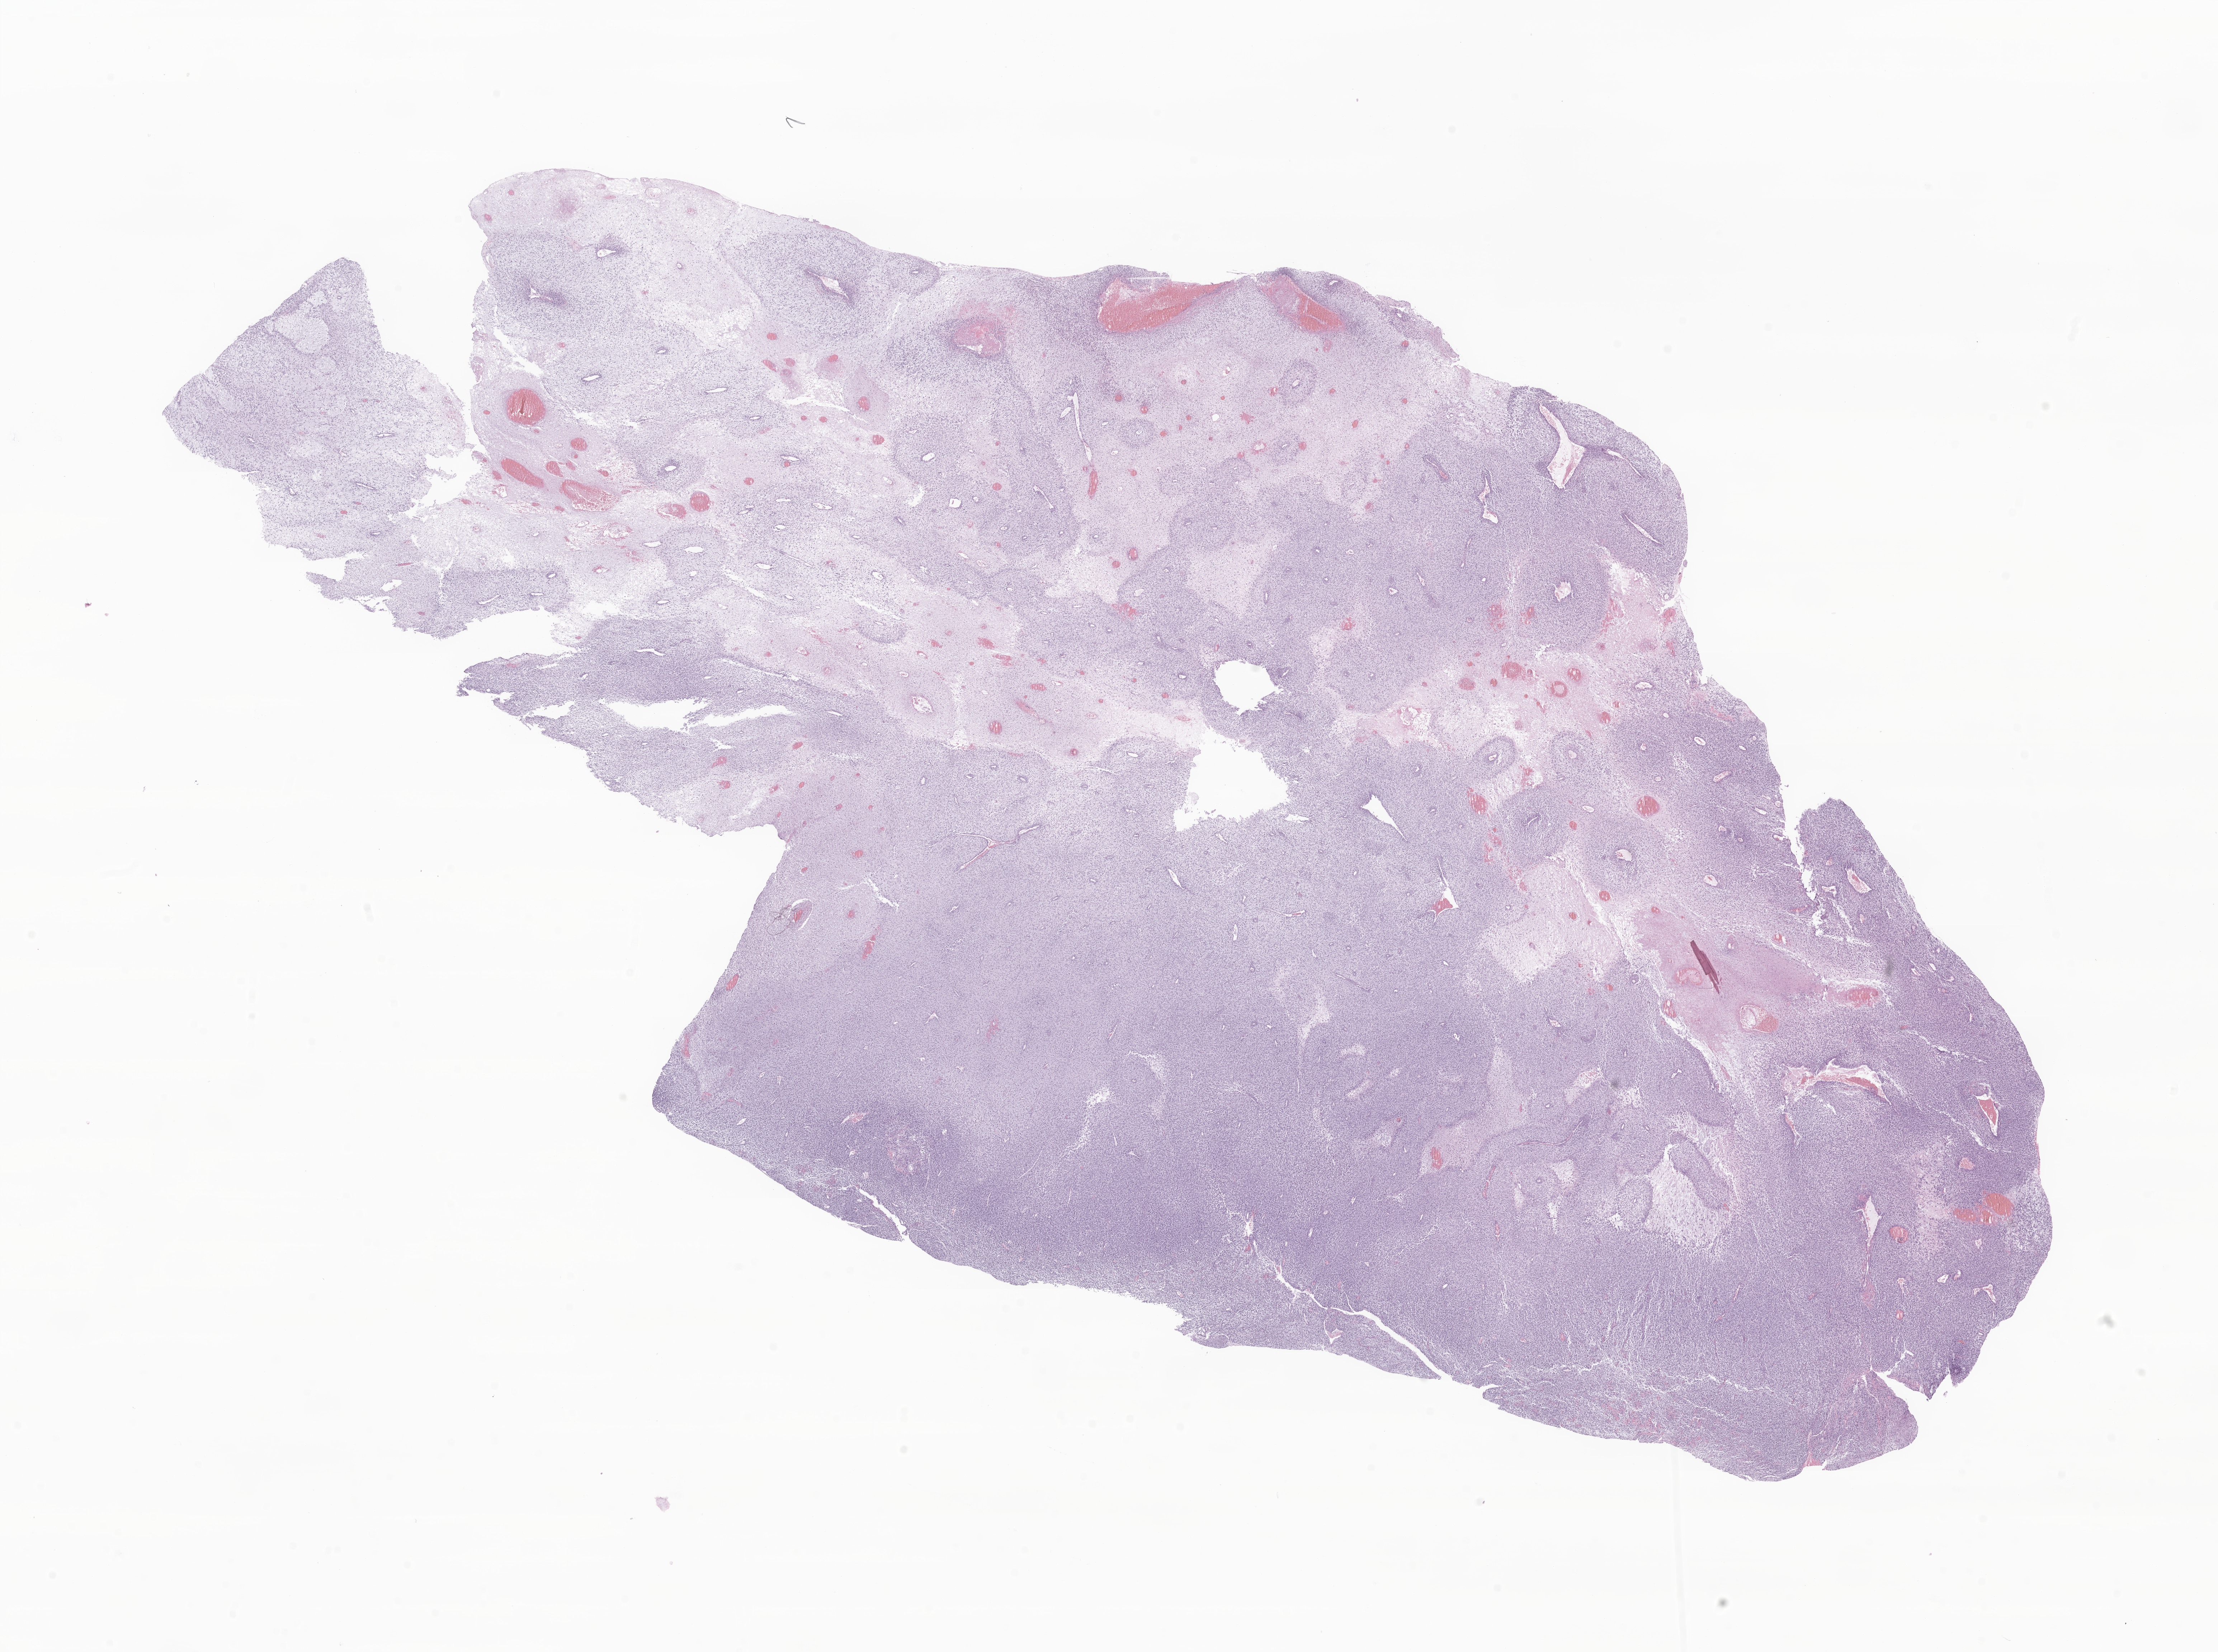
Hematoxylin and eosin (H&E) whole-slide image of tumor tissue from the soft tissue of lower extremity, shown as a low-resolution overview of the whole scanned area (about 26.1 x 19.4 mm); FFPE section. Patient: female, age 186 months (15 years 6 months).
Diagnosis (ICD-O-3 morphology term): Sarcoma, NOS. Tissue or organ of origin (case record): connective, subcutaneous and other soft tissues of lower limb and hip.